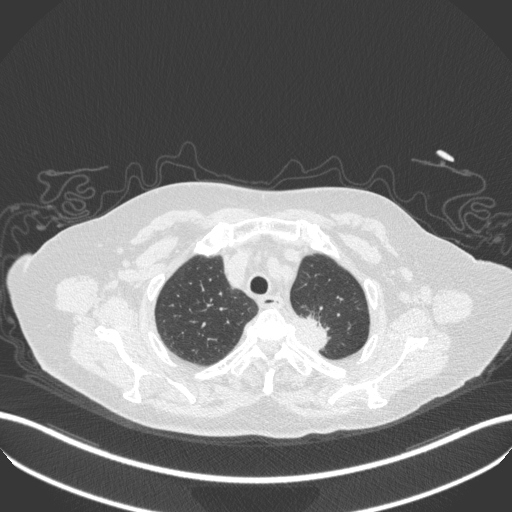
Chest CT, one axial slice. Position 288 of 353 along the scan axis. 100 kVp. Lung window (W 1500 / L -600 HU). 1 mm slice thickness. 512 × 512 image matrix. Female patient, age 81 years. From the clinical record (not read from this slice): clinical TNM (as recorded): T2a N0 M0.
Outlined on this slice (bounding box drawn by a radiologist):
- lung tumour (recorded histology: adenocarcinoma): bounding box <285,315,339,357> (left, top, right, bottom; pixels)